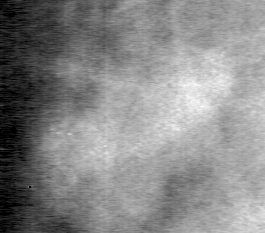
Region of interest cut from a scanned film mammogram (one marked finding), left breast, MLO view.
Mass, shape lobulated, margins circumscribed; BI-RADS assessment category 4; pathology result (as recorded, not read from the image): benign.